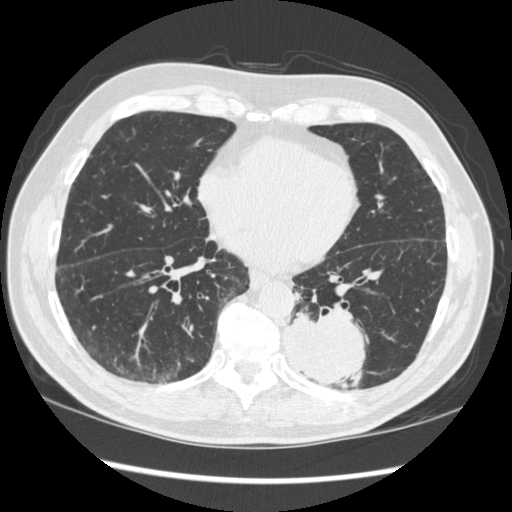
Low-dose screening chest CT, one axial slice; position 127 of 348 along the scan axis; reconstruction kernel STANDARD; lung window (W 1500 / L -600 HU); 1.25 mm slice thickness; 512 × 512 image matrix.
Outlined on this slice (manually delineated by an expert):
- lesion 1 (tumor, lower lobe of left lung): bounding box <284,311,366,389> (left, top, right, bottom; pixels)